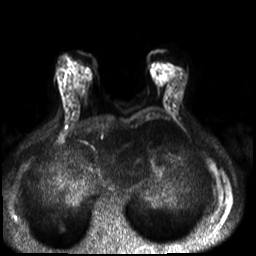
Breast MRI, one axial slice. Diffusion-weighted series; image 2 of 4 stored at this slice position (different b-values; order by instance number). 3 T. 4 mm slice thickness. 256 × 256 image matrix, field of view 320 × 320 mm. Female patient.
Annotated regions visible in this slice (manually delineated by an expert):
- tumour on diffusion-weighted imaging: bounding box [x1, y1, x2, y2] px = [84, 68, 91, 79]